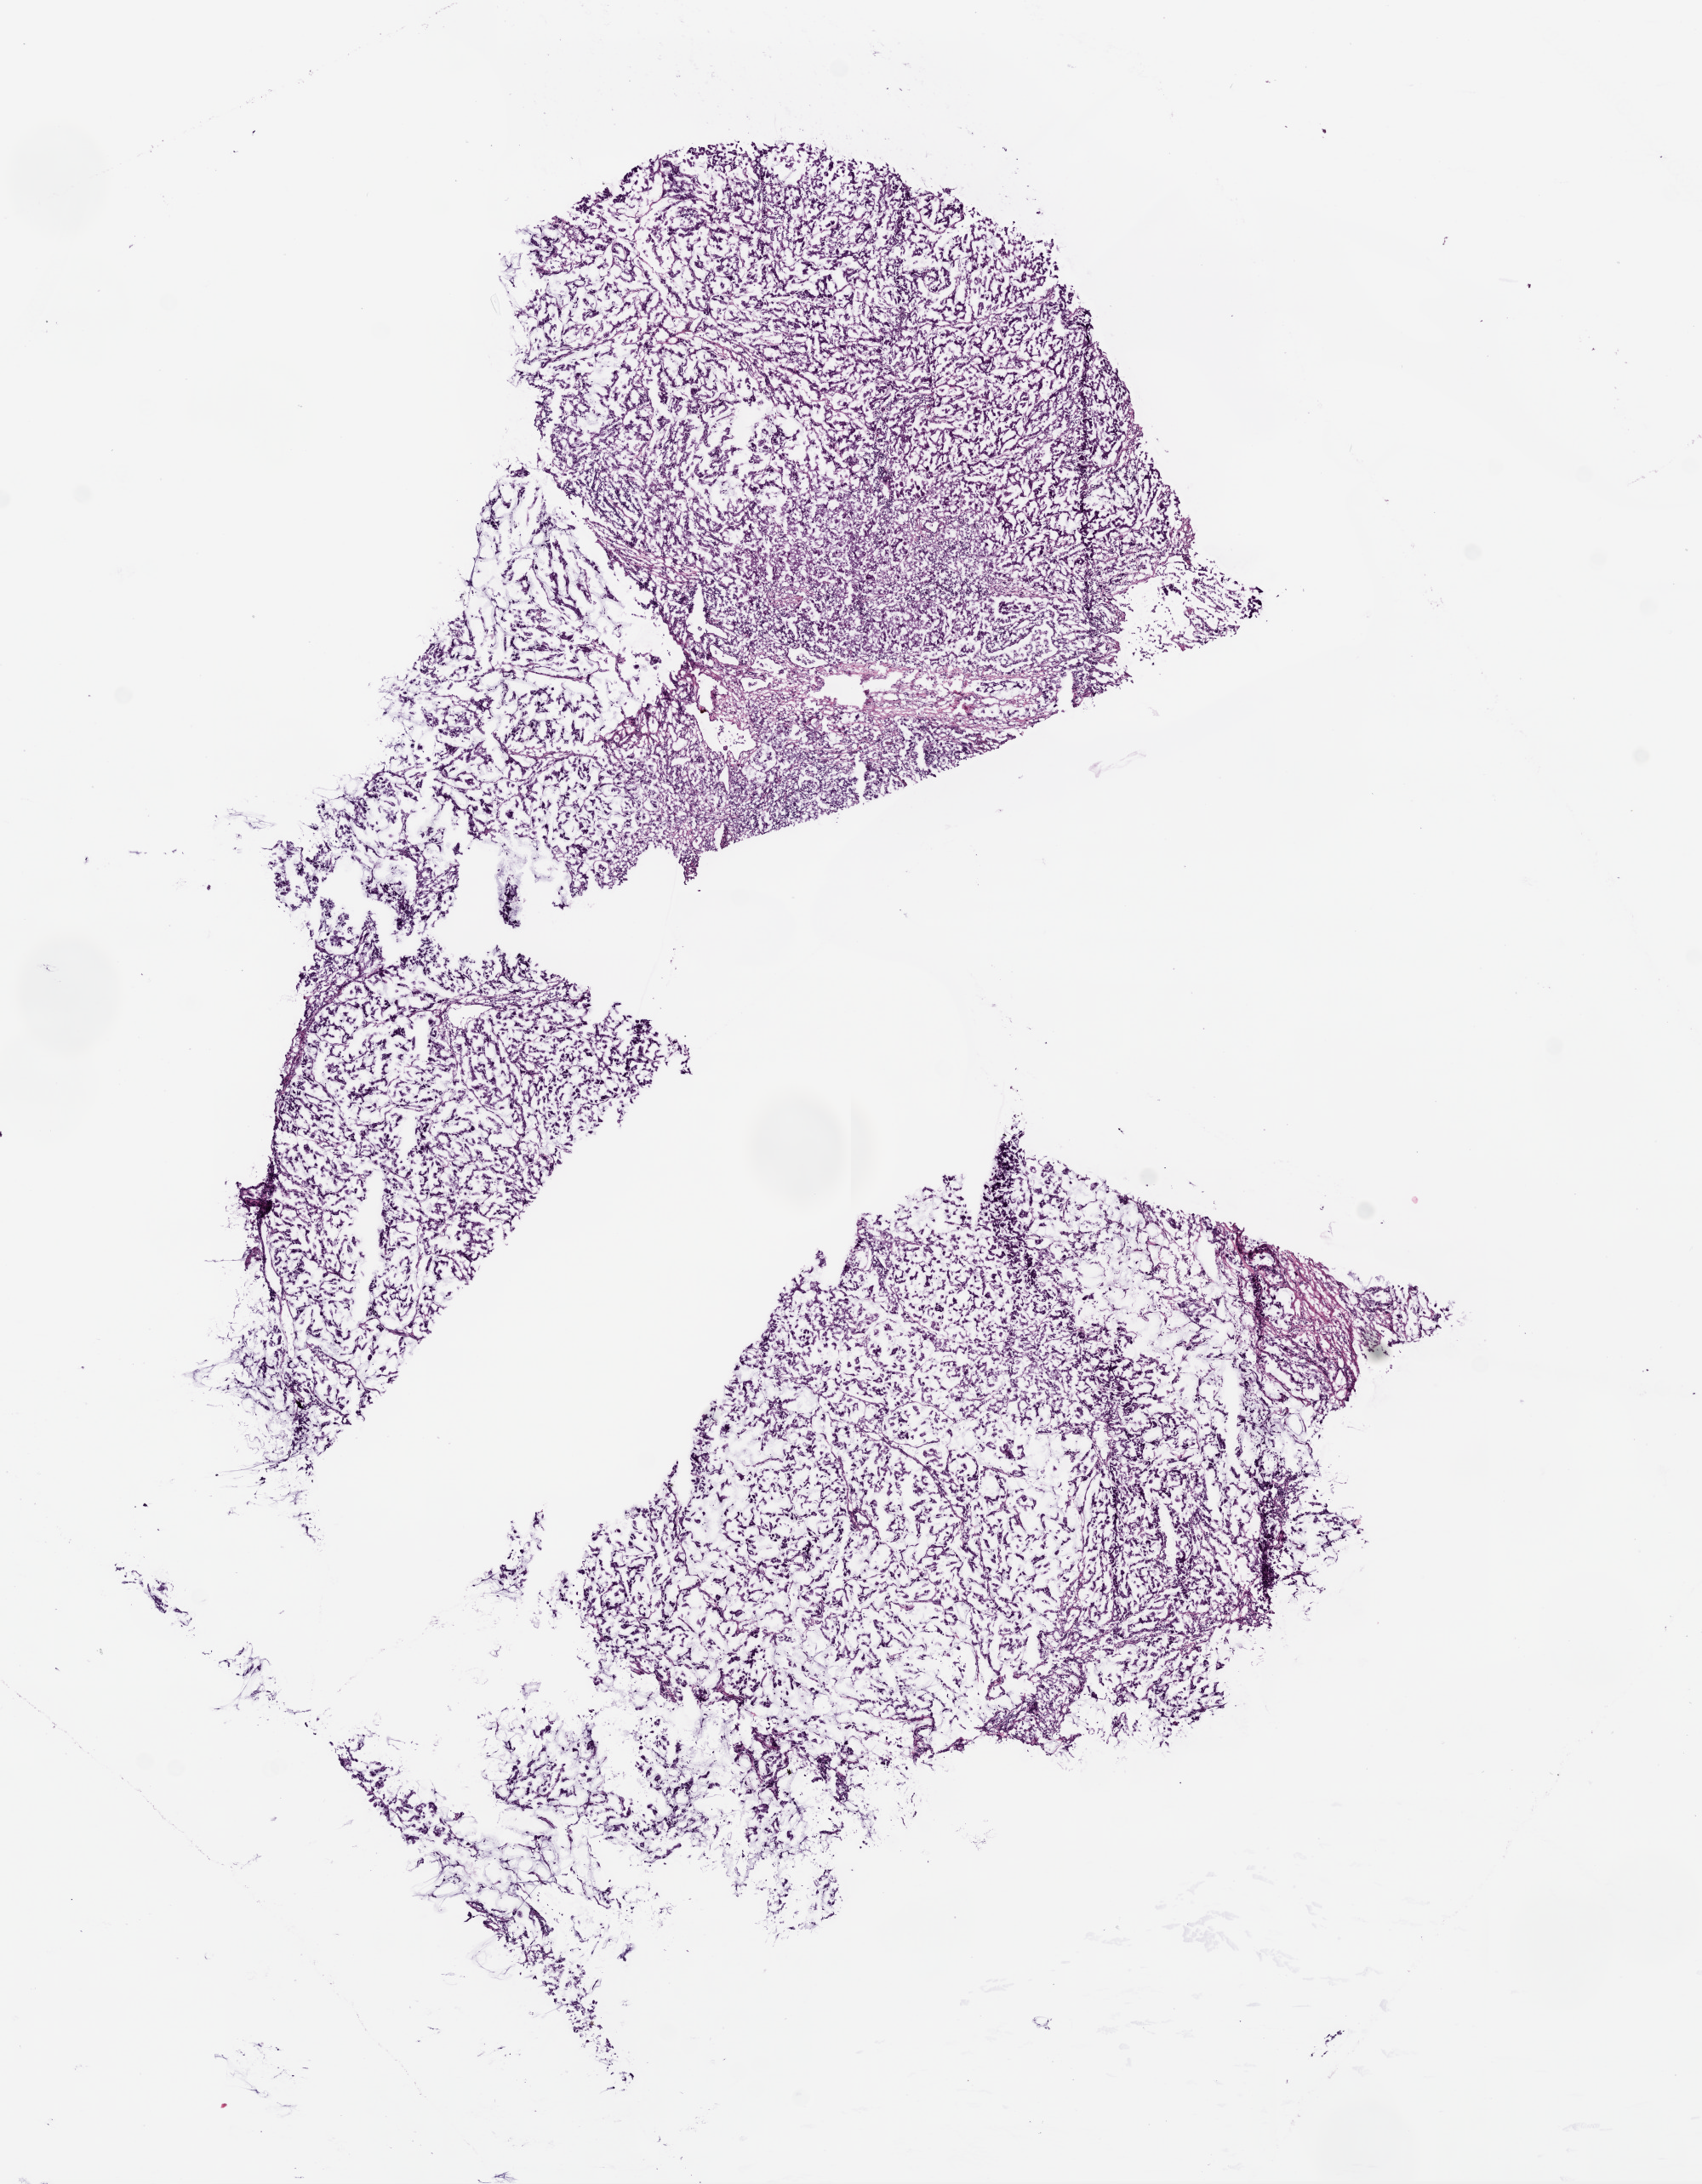
Whole-slide histology image, Hematoxylin and eosin (H&E) stained, a low-resolution overview of the entire scanned area, about 8.0 x 10.3 mm (from a 20x scan); frozen section from the bottom of the tissue portion; primary tumour sample from the lung. Female, age 68 years at initial diagnosis. Slide review estimates, as recorded: tumour cells 95%, tumour nuclei 75%, normal cells 0%, stromal cells 5%, necrosis 0%.
AJCC pathologic stage: IIB (4th edition). Histologic diagnosis: Adenocarcinoma, NOS (upper lobe, lung).